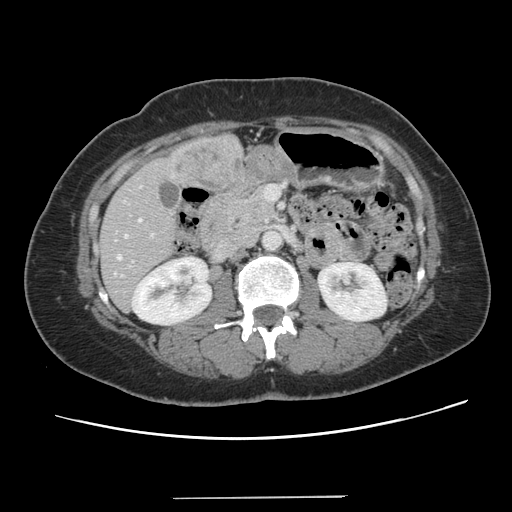
Contrast-enhanced abdominal CT, one axial slice; position 52 of 141 along the scan axis; 120 kVp; intravenous contrast given; soft-tissue window (W 400 / L 40 HU); 512 × 512 image matrix, field of view 366 × 366 mm. Female patient, age 53 years. From the clinical record (not read from this slice): diagnosis: colorectal cancer liver metastases, imaged before liver resection; multiple liver metastases: no; largest metastasis: 14.5 cm; disease in both lobes: yes.
Outlined on this slice (outlined manually by an expert reader):
- hepatic veins: bounding box <117,234,126,259> (left, top, right, bottom; pixels)
- liver: <99,136,242,310>
- planned liver remnant (the part of the liver to remain after resection): <98,218,177,310>
- portal vein (with intrahepatic branches): <139,219,153,235>
- liver metastasis: <175,142,239,187>